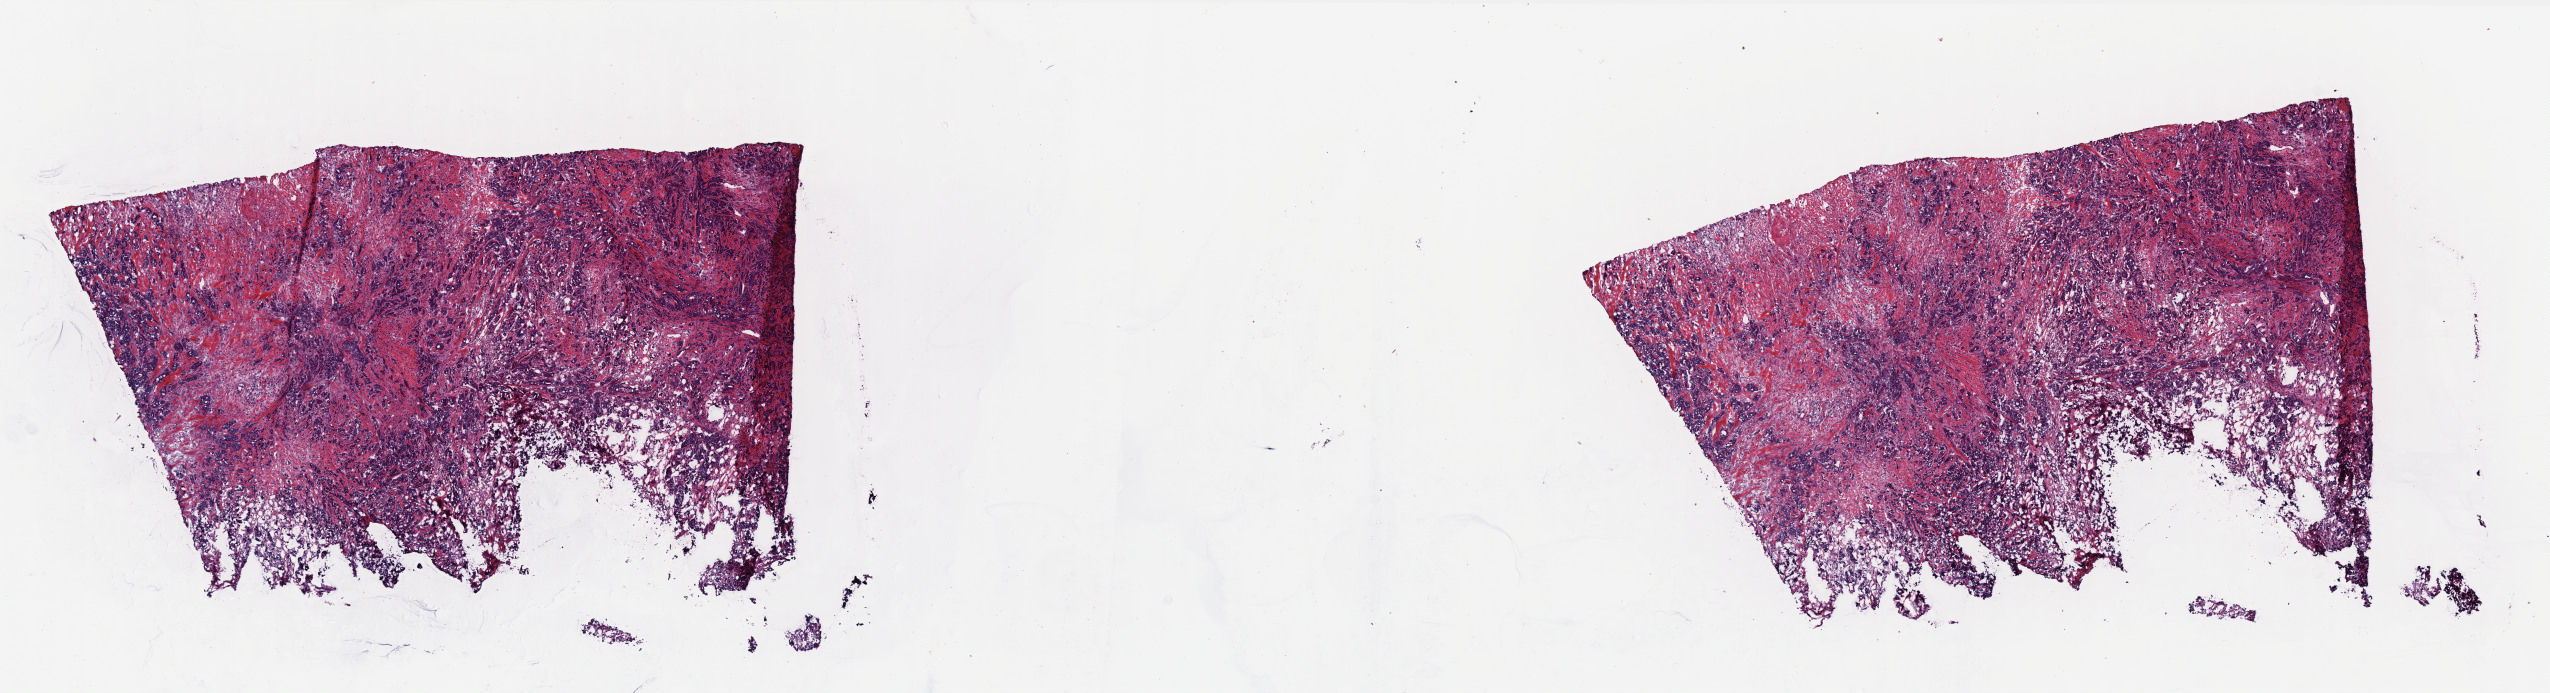
Whole-slide histology image, H&E-stained, shown as a low-resolution overview of the whole scanned area (about 20.4 x 5.6 mm); frozen section; breast, primary tumour sample. Female patient; age at initial diagnosis 70 years. Composition of this section per pathologist review: tumour cells 65%, tumour nuclei 73%, normal cells 3%, stromal cells 28%, necrosis 4%. Inflammatory infiltration, as recorded: lymphocyte infiltration 13%, monocyte infiltration 0%, neutrophil infiltration 0%.
AJCC pathologic stage: IIIA. Histologic diagnosis: Infiltrating duct carcinoma, NOS.